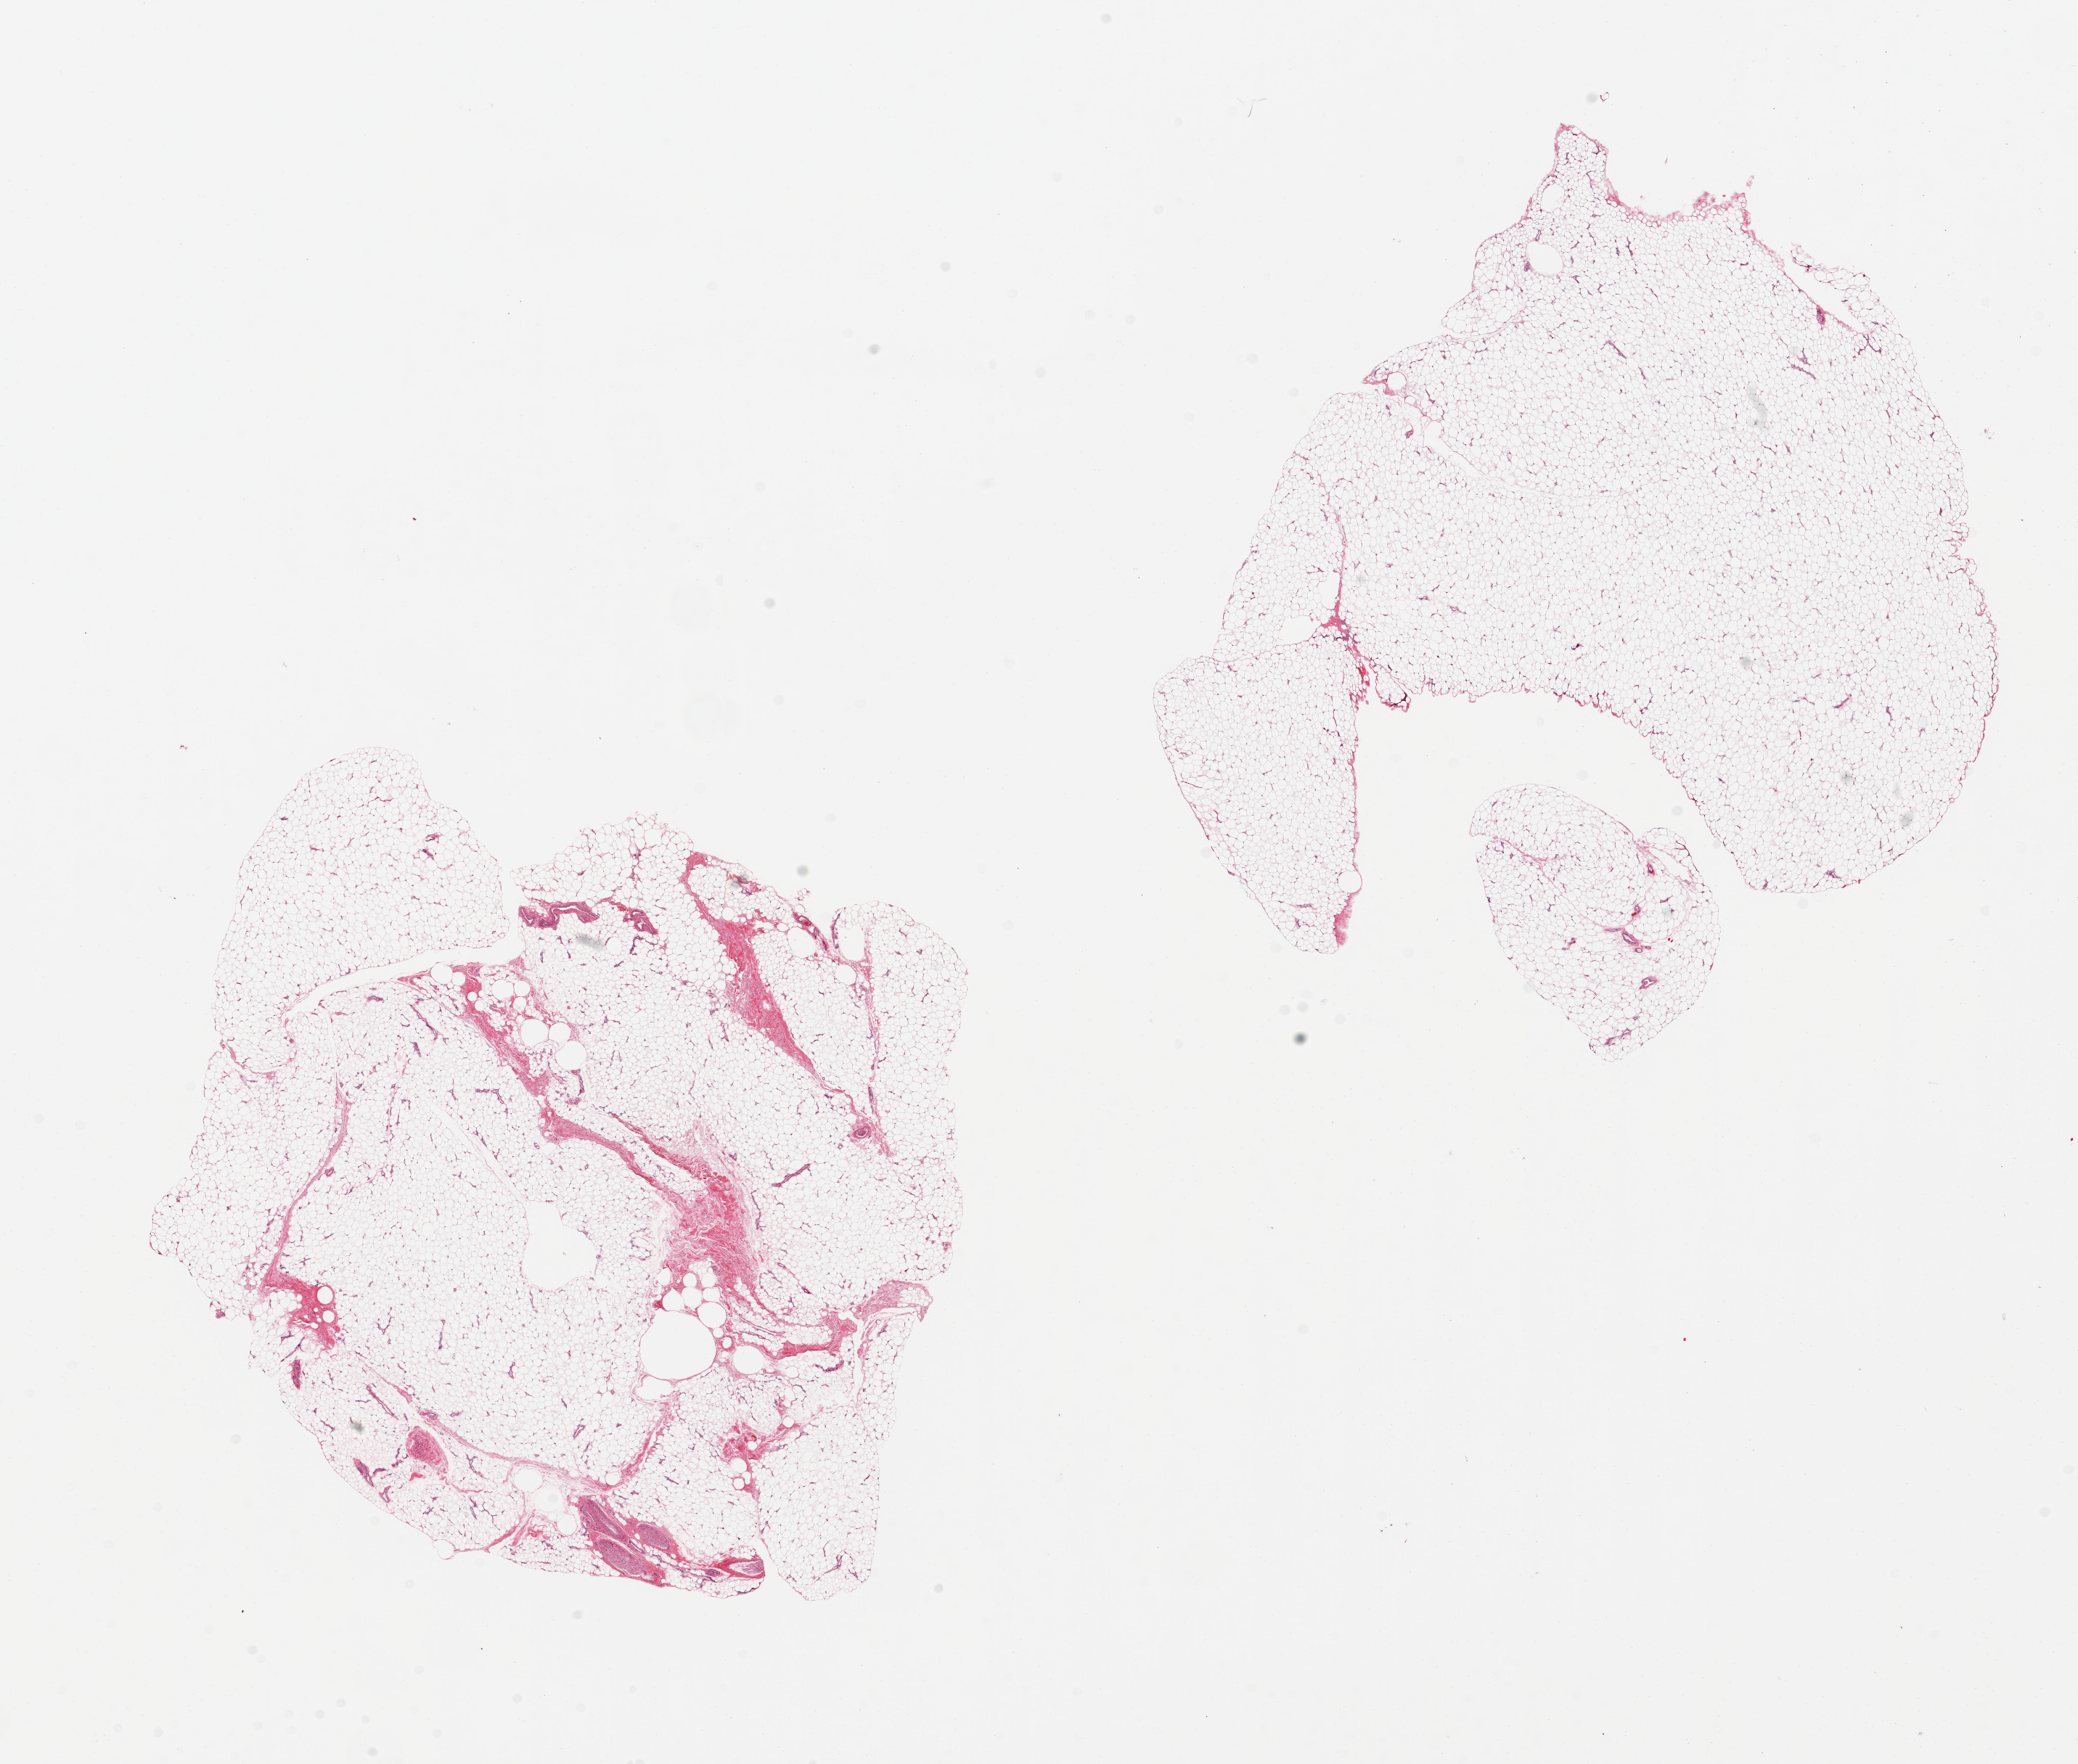
Digitized H&E-stained section, brightfield, low-resolution overview of the scanned area, about 22.6 x 19.2 mm, PAXgene-fixed paraffin-embedded (PFPE) section, section of adipose tissue (target tissue), donor tissue sample. Donor sex: male.
Reviewer comment on this tissue sample: 2 pieces.